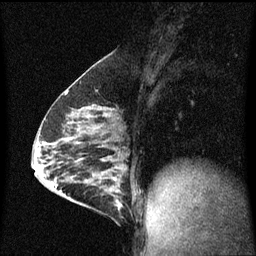
Breast MRI (dynamic contrast-enhanced), one sagittal slice. Slice 32 of 60 in the series (ordered by position). Dynamic contrast-enhanced series, image 2 of 3 at this slice position (ordered by acquisition). 1.5 T. TE 4.2 ms, TR 8 ms. 2 mm slice thickness. 256 × 256 image matrix, field of view 200 × 200 mm. Female patient, age 64 years.
Structures marked on this image (semi-automatic segmentation, software-assisted and operator-edited):
- analysis volume of interest (the breast-tissue region the enhancement analysis was run in; not a lesion): bounding box (x1, y1, x2, y2) in pixels: (87, 176, 124, 217)
- tumour enhancement mask (voxels above the 70 % enhancement threshold inside the analysis volume of interest): (92, 176, 122, 211)